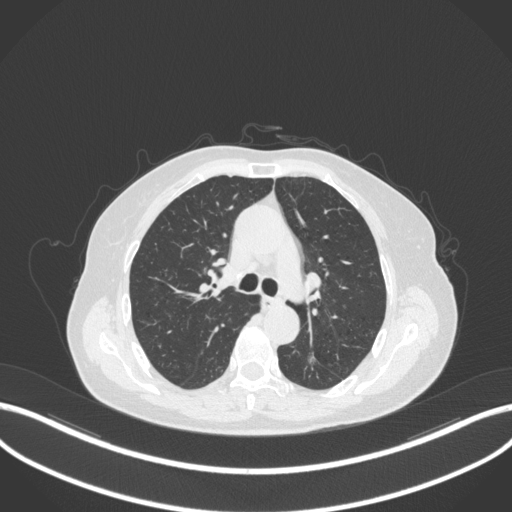
Chest CT, one axial slice. Slice 199 of 352 in the series (ordered by position). 120 kVp. Lung window (W 1500 / L -600 HU). 512 × 512 image matrix. Female patient, age 70 years. Case-level facts recorded for this patient, not image findings: clinical TNM (as recorded): T1c N0 M0.
Outlined on this slice (rectangle marked by the reading radiologist):
- lung tumour (recorded histology: adenocarcinoma): bounding box (x1, y1, x2, y2) in pixels: (303, 350, 323, 368)